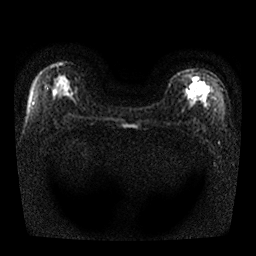
Breast MRI, one axial slice; position 16 of 25 along the scan axis; diffusion-weighted series; image 2 of 4 stored at this slice position (different b-values; order by instance number); 1.5 T; 4 mm slice thickness; 256 × 256 image matrix, field of view 330 × 330 mm. Female patient.
Outlined on this slice (expert manual segmentation):
- tumour on diffusion-weighted imaging: bounding box [x1, y1, x2, y2] px = [188, 83, 195, 88]